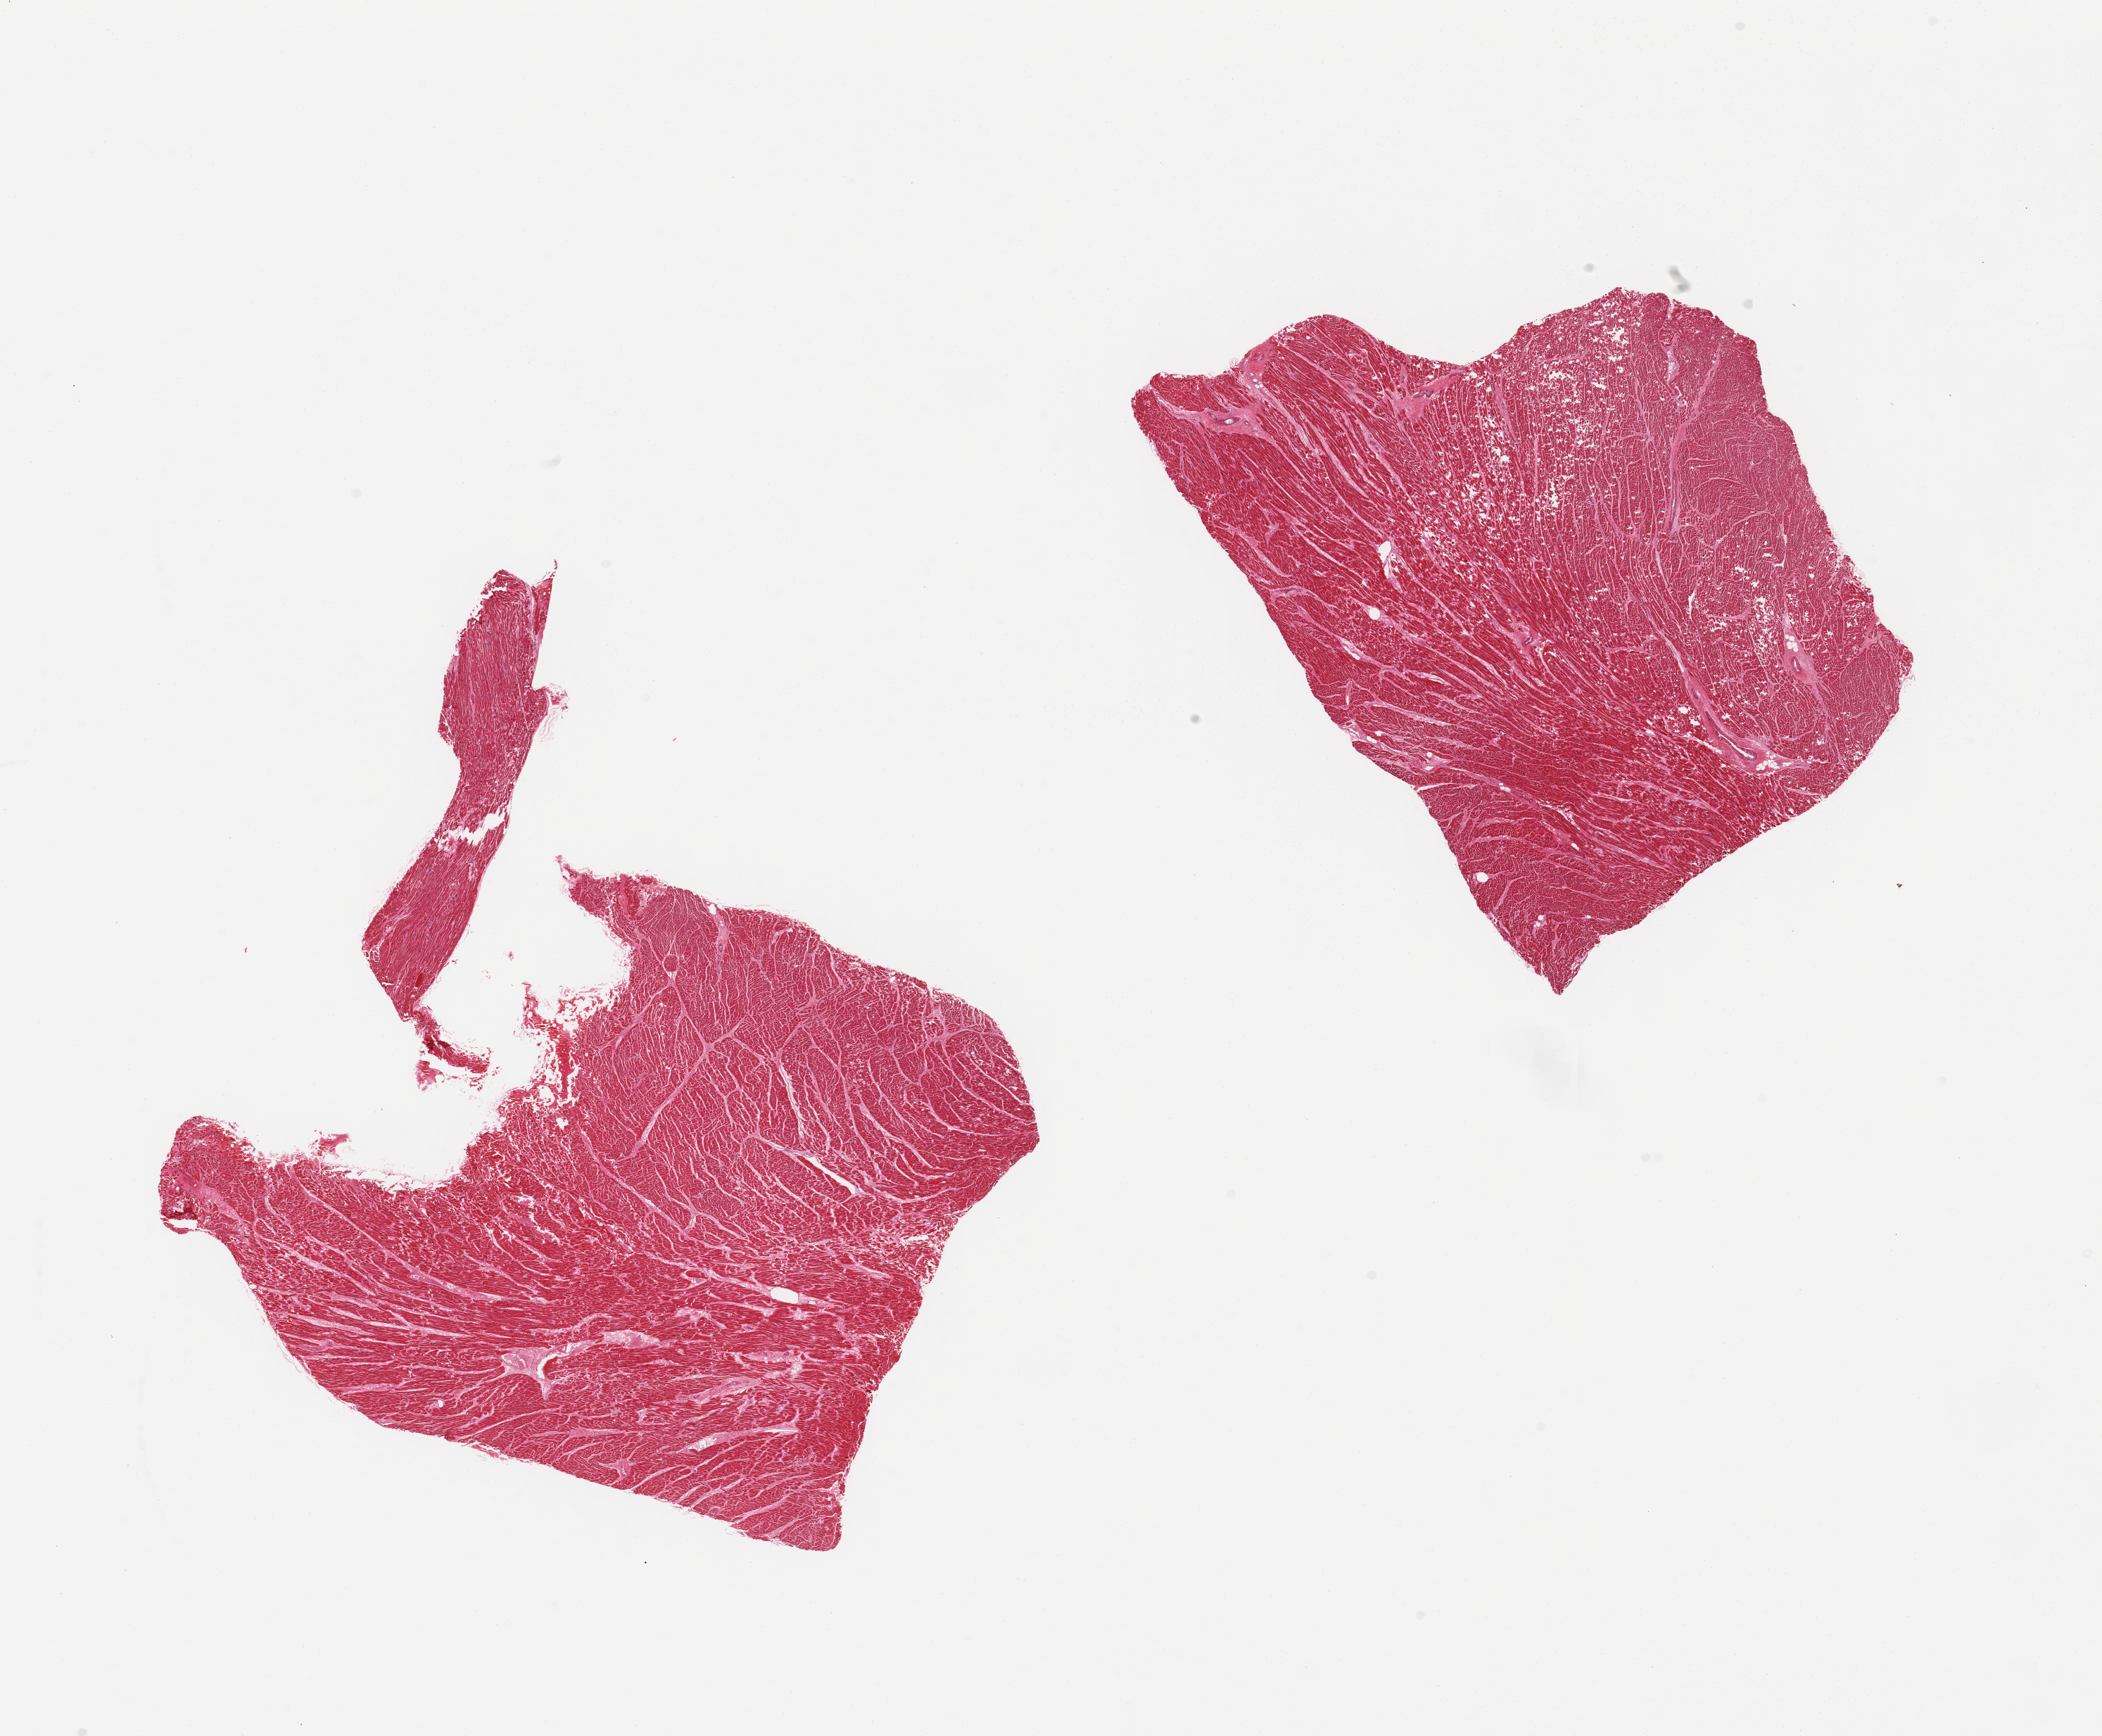
Haematoxylin and eosin whole-slide image — a low-resolution overview of the entire scanned area, about 23.6 x 19.5 mm; PAXgene-fixed, paraffin-embedded tissue; sampled site (target tissue): heart; tissue donor sample. Male donor.
Pathologist's review note for this sample: 2 pieces; fragmented myofibers.